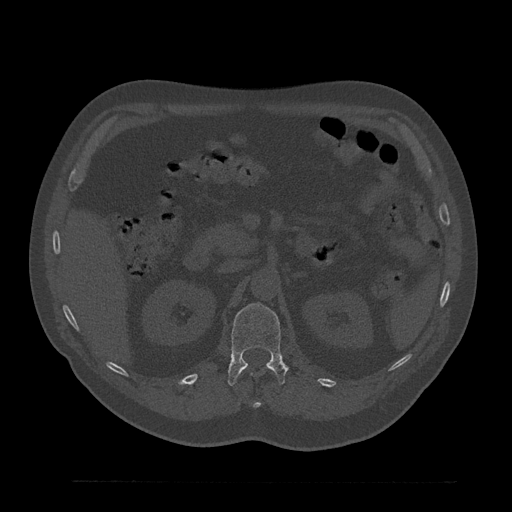
CT including the spine, one axial slice; slice 183 of 797 in the series (ordered by position); bone window (W 1800 / L 400 HU); 512 × 512 image matrix, field of view 430 × 430 mm. Male patient, age 61 years. From the clinical record (not read from this slice): primary cancer: prostate.
Structures marked on this image (semi-automatic segmentation, software-assisted and operator-edited):
- L1 vertebra: bounding box <227,303,288,386> (left, top, right, bottom; pixels)
- T12 vertebra: <253,402,261,408>